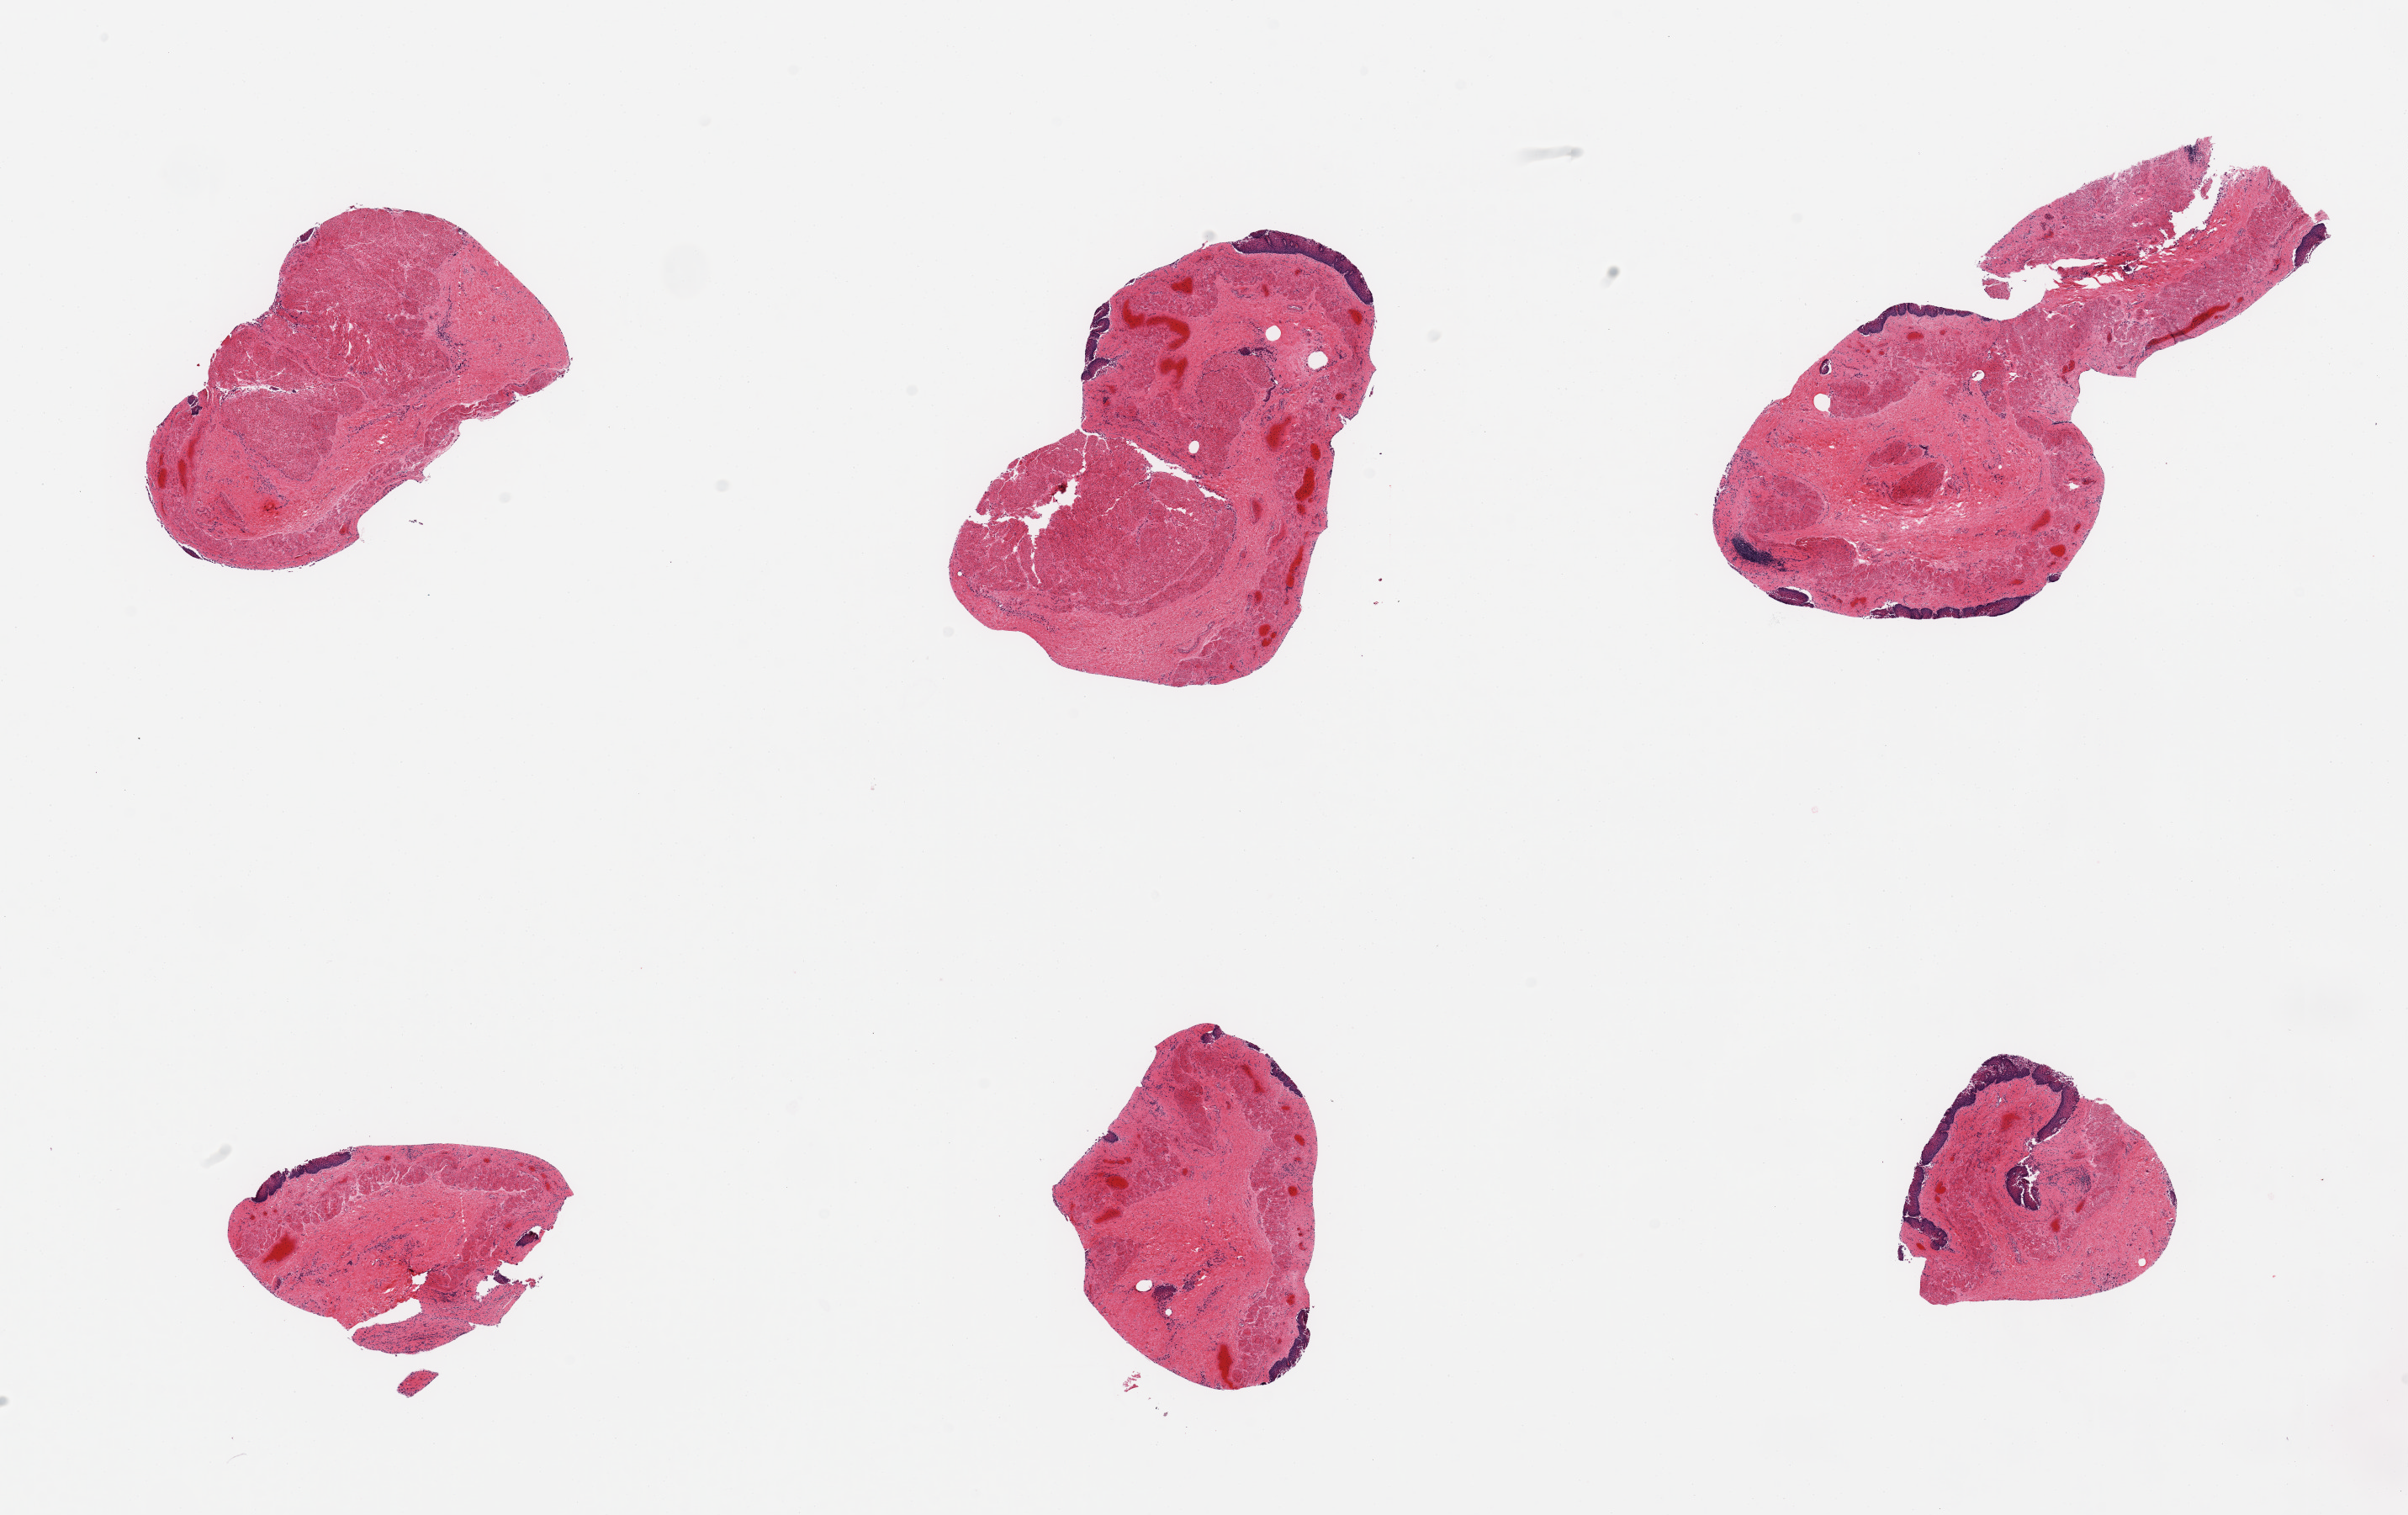
Haematoxylin and eosin whole-slide image — shown as a low-resolution overview of the whole scanned area (about 22.6 x 14.2 mm), PAXgene-fixed paraffin-embedded (PFPE) section, target tissue: esophageal mucous membrane, tissue donor sample. Donor: female.
Reviewer comment on this tissue sample: 6 pieces; squamous epithelium is largely sloughed, ? portion of muscularis.